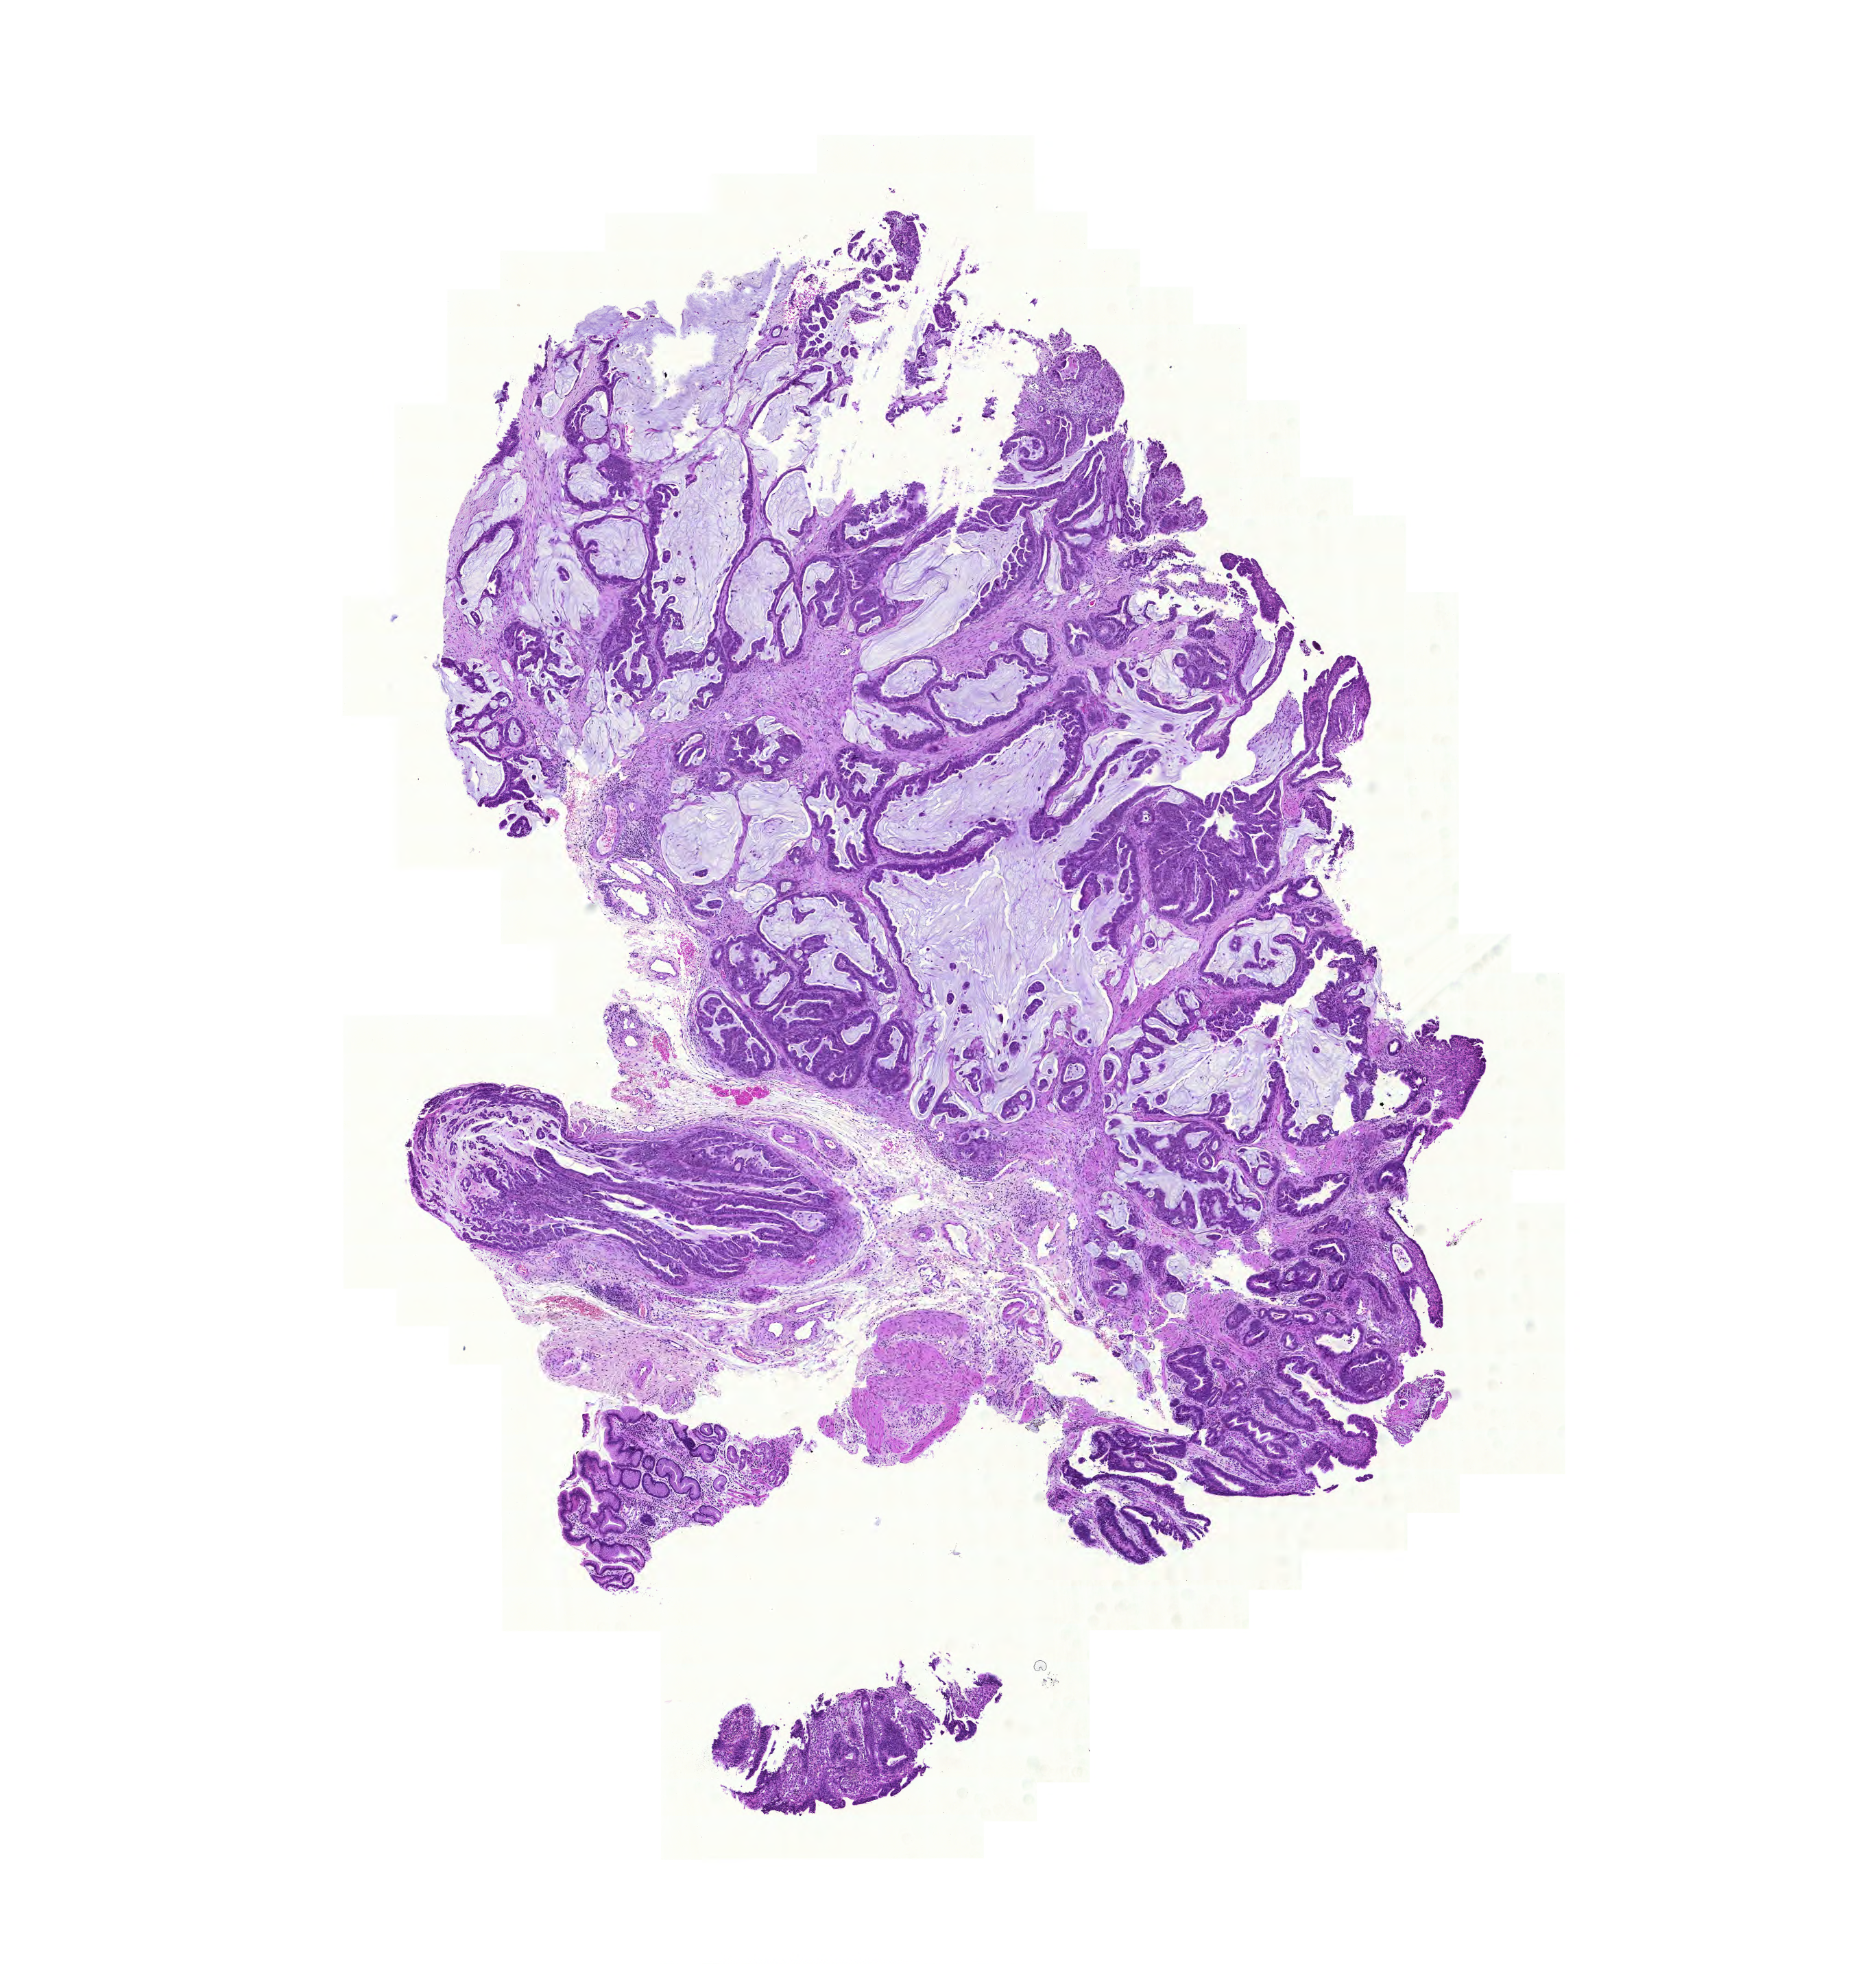
Digitized H&E tissue section (whole slide) — shown as a low-resolution overview of the whole scanned area (about 10.2 x 10.7 mm). Formalin-fixed paraffin-embedded (FFPE) diagnostic section. Sample: primary tumour, stomach. Patient: male, age at initial diagnosis 81 years. Histologic grade: G2 (moderately differentiated).
Lymph nodes positive (case pathology): 6 of 42 examined. Pathologic diagnosis: Mucinous adenocarcinoma (gastric antrum). AJCC pathologic stage: II (5th edition).